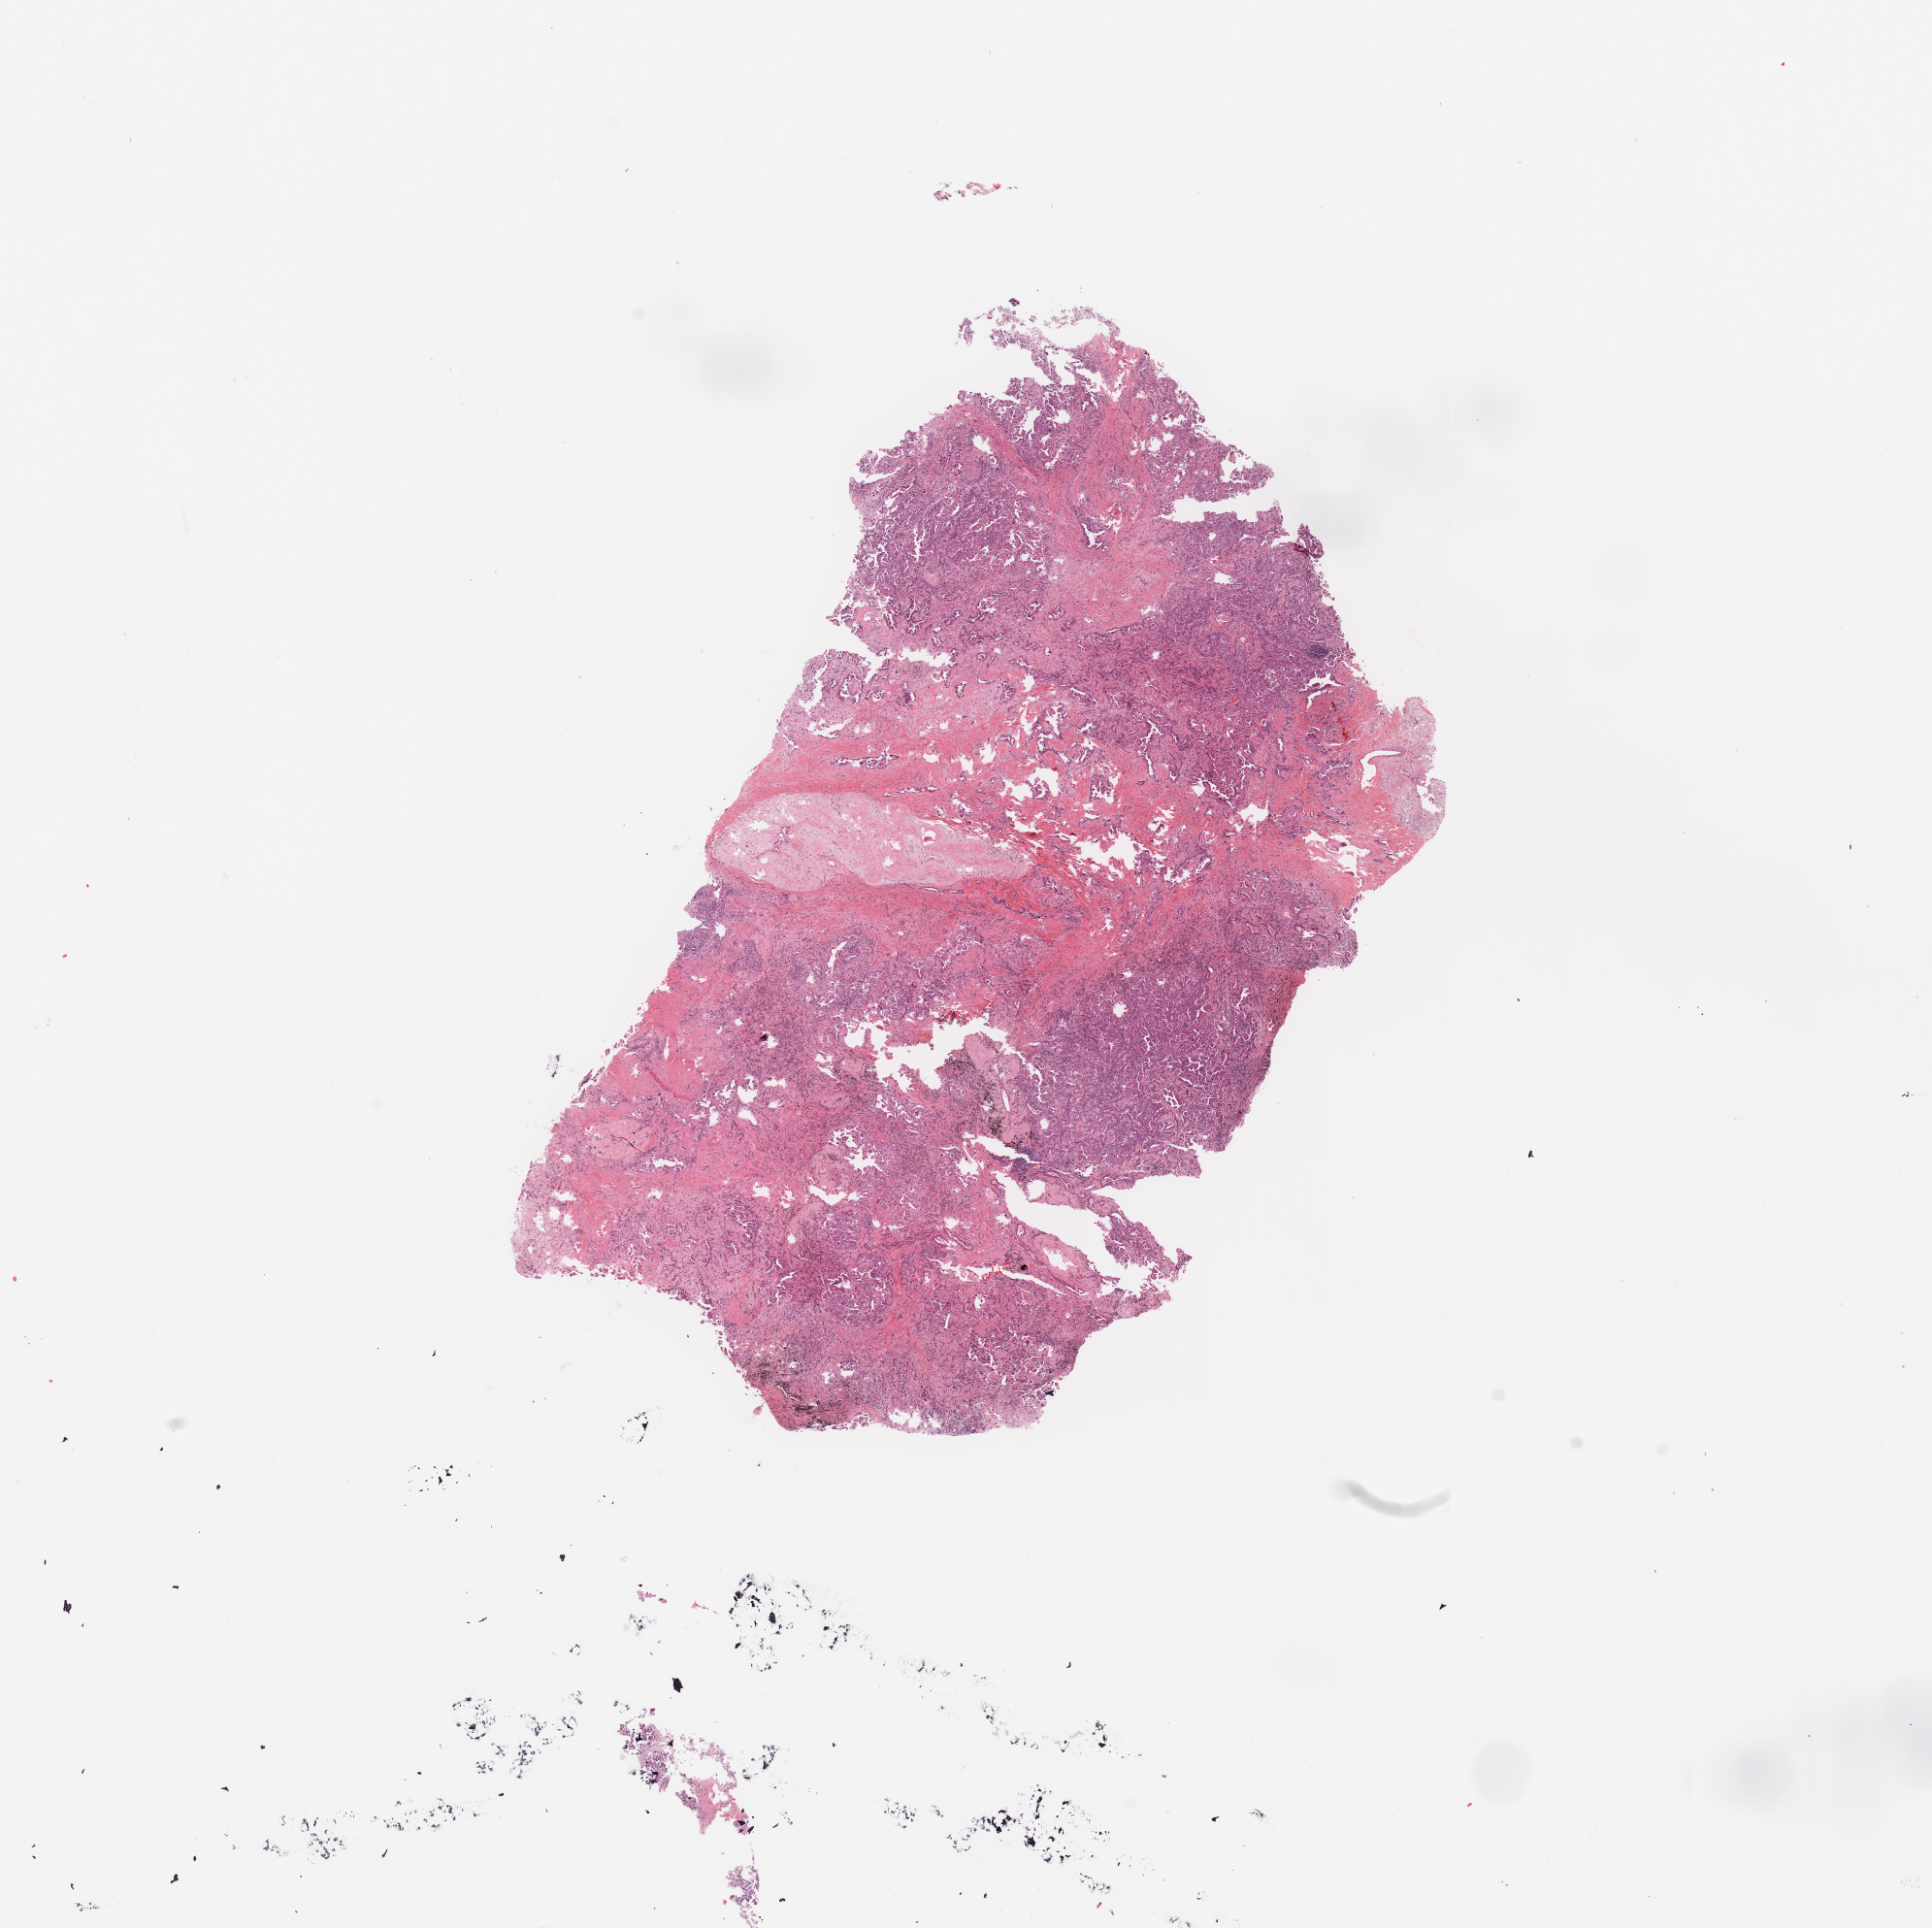
Whole-slide histology image, H&E-stained — shown as a low-resolution overview of the whole scanned area (about 15.8 x 15.7 mm), tumour tissue sample, sampled site: lung. 79-year-old female patient. Histologic grade: G3 (poorly differentiated). Composition of this section per pathologist review: tumour nuclei 65%, necrosis 5%.
Histologic diagnosis: Adenocarcinoma, NOS. AJCC pathologic stage: IIA. Primary tumour site (as recorded): right middle lobe.